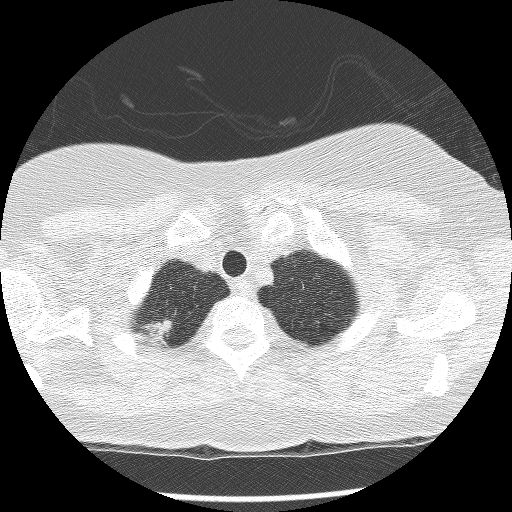
Axial slice from a low-dose chest CT screening exam, second annual screen, lung window (W 1500 / L -600 HU), 2.5 mm slice thickness, slice 14 of 136 in the series, 512 × 512 image matrix, field of view 320 × 320 mm. Female, age 56 years at enrolment.
• Lesion marked by an expert reader, bounding box (x1, y1, x2, y2) in pixels: (132, 309, 184, 357).
• Screening reader's record for this exam: no non-calcified nodule ≥4 mm recorded.
• Lung cancer was diagnosed 366 days after this screen: large cell carcinoma, NOS, right upper lobe, poorly differentiated (G3), stage IB (AJCC 6th edition), 15 mm at pathology.